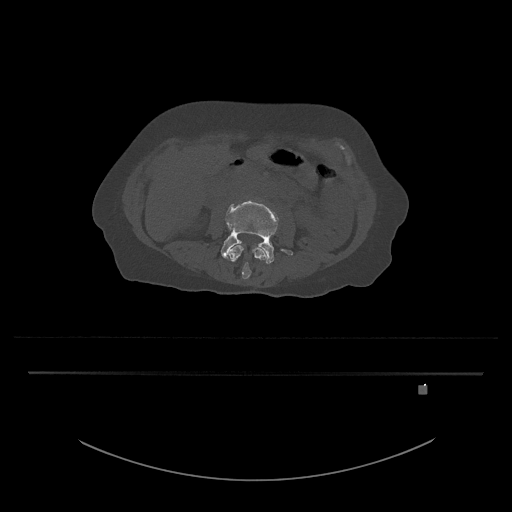
CT including the spine, one axial slice. Position 389 of 797 along the scan axis. Reconstruction kernel Br40s/3. Bone window (W 1800 / L 400 HU). 0.5 mm slice thickness. 512 × 512 image matrix. Female patient, age 57 years. From the clinical record (not read from this slice): primary cancer: cervical.
Annotated regions visible in this slice (semi-automatically segmented with operator editing):
- L3 vertebra: box from (x=228, y=245) to (x=268, y=279) px
- L4 vertebra: (x=221, y=201)–(x=293, y=264)